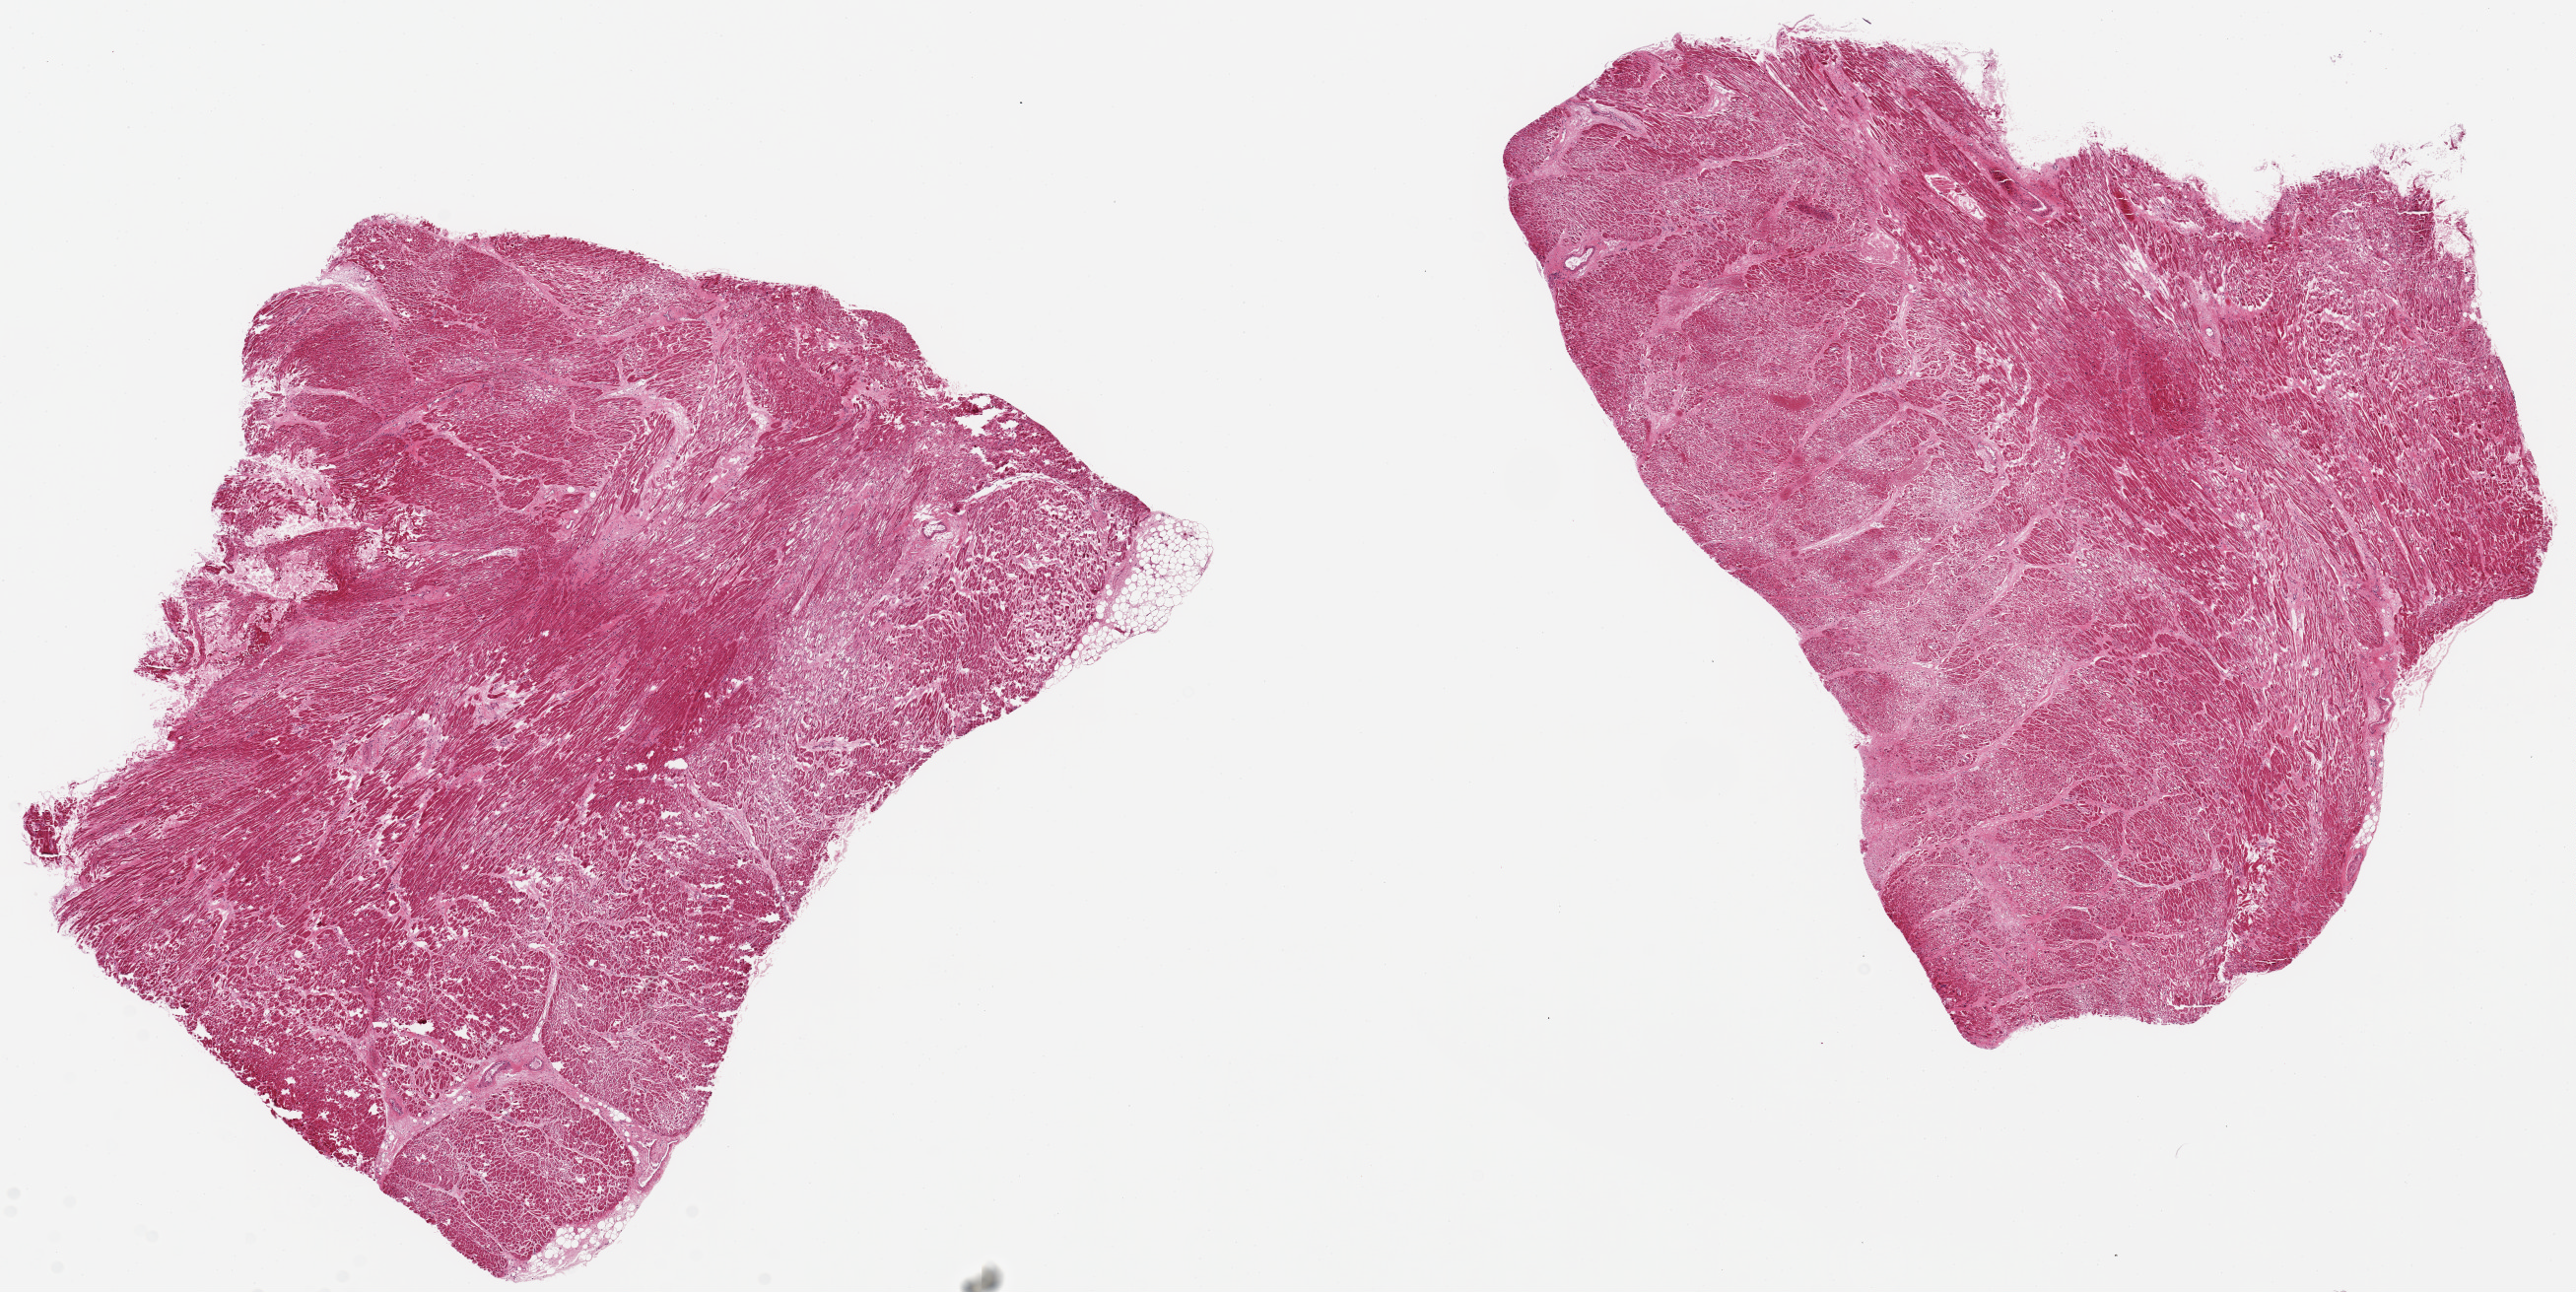
Whole-slide image, hematoxylin and eosin (H&E) stain — shown as a low-resolution overview of the whole scanned area (about 20.7 x 10.4 mm, slide scanned at 20x). PAXgene-fixed, paraffin-embedded tissue. Sampled site (target tissue): heart. Tissue donor sample. Donor: female.
Reviewer comment on this tissue sample: 2 pieces, 8x7 & 9x8mm; hypertrophied fibers.